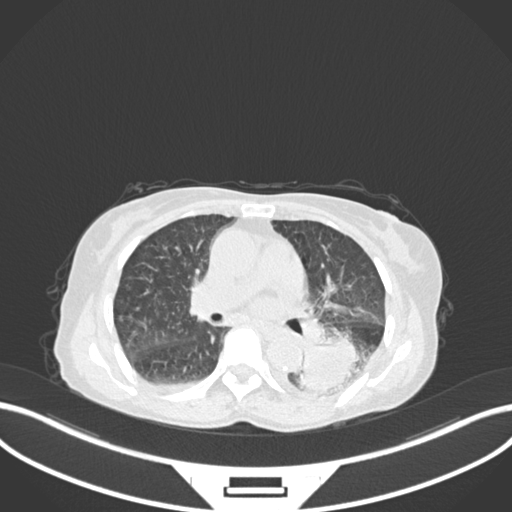
Chest CT, one axial slice. Reconstruction kernel B30f. 120 kVp. Lung window (W 1500 / L -600 HU). 512 × 512 image matrix. Female patient, age 78 years. Case-level facts recorded for this patient, not image findings: clinical TNM (as recorded): T3 N0 M1.
Outlined on this slice (rectangle marked by the reading radiologist):
- lung tumour (recorded histology: squamous cell carcinoma): bounding box [x1, y1, x2, y2] px = [297, 335, 365, 396]